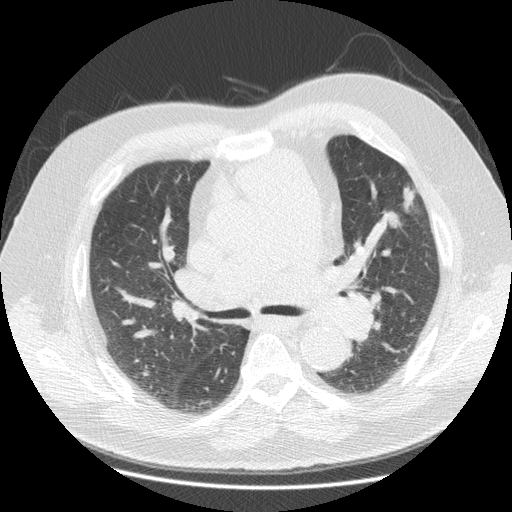
Axial slice from a low-dose chest CT screening exam; second annual screen; lung window (W 1500 / L -600 HU); 140 kVp; slice 65 of 116 in the series; 512 × 512 image matrix. Male participant, aged 67 years at enrolment. Former smoker at enrolment.
Expert-annotated lung lesion, bounding box [x1, y1, x2, y2] px = [374, 173, 433, 241]. The screening reader recorded 3 non-calcified nodules or masses ≥4 mm on this exam (left upper lobe, left upper lobe, left upper lobe); which of them this box marks is not recorded. Official screen result: positive, other.